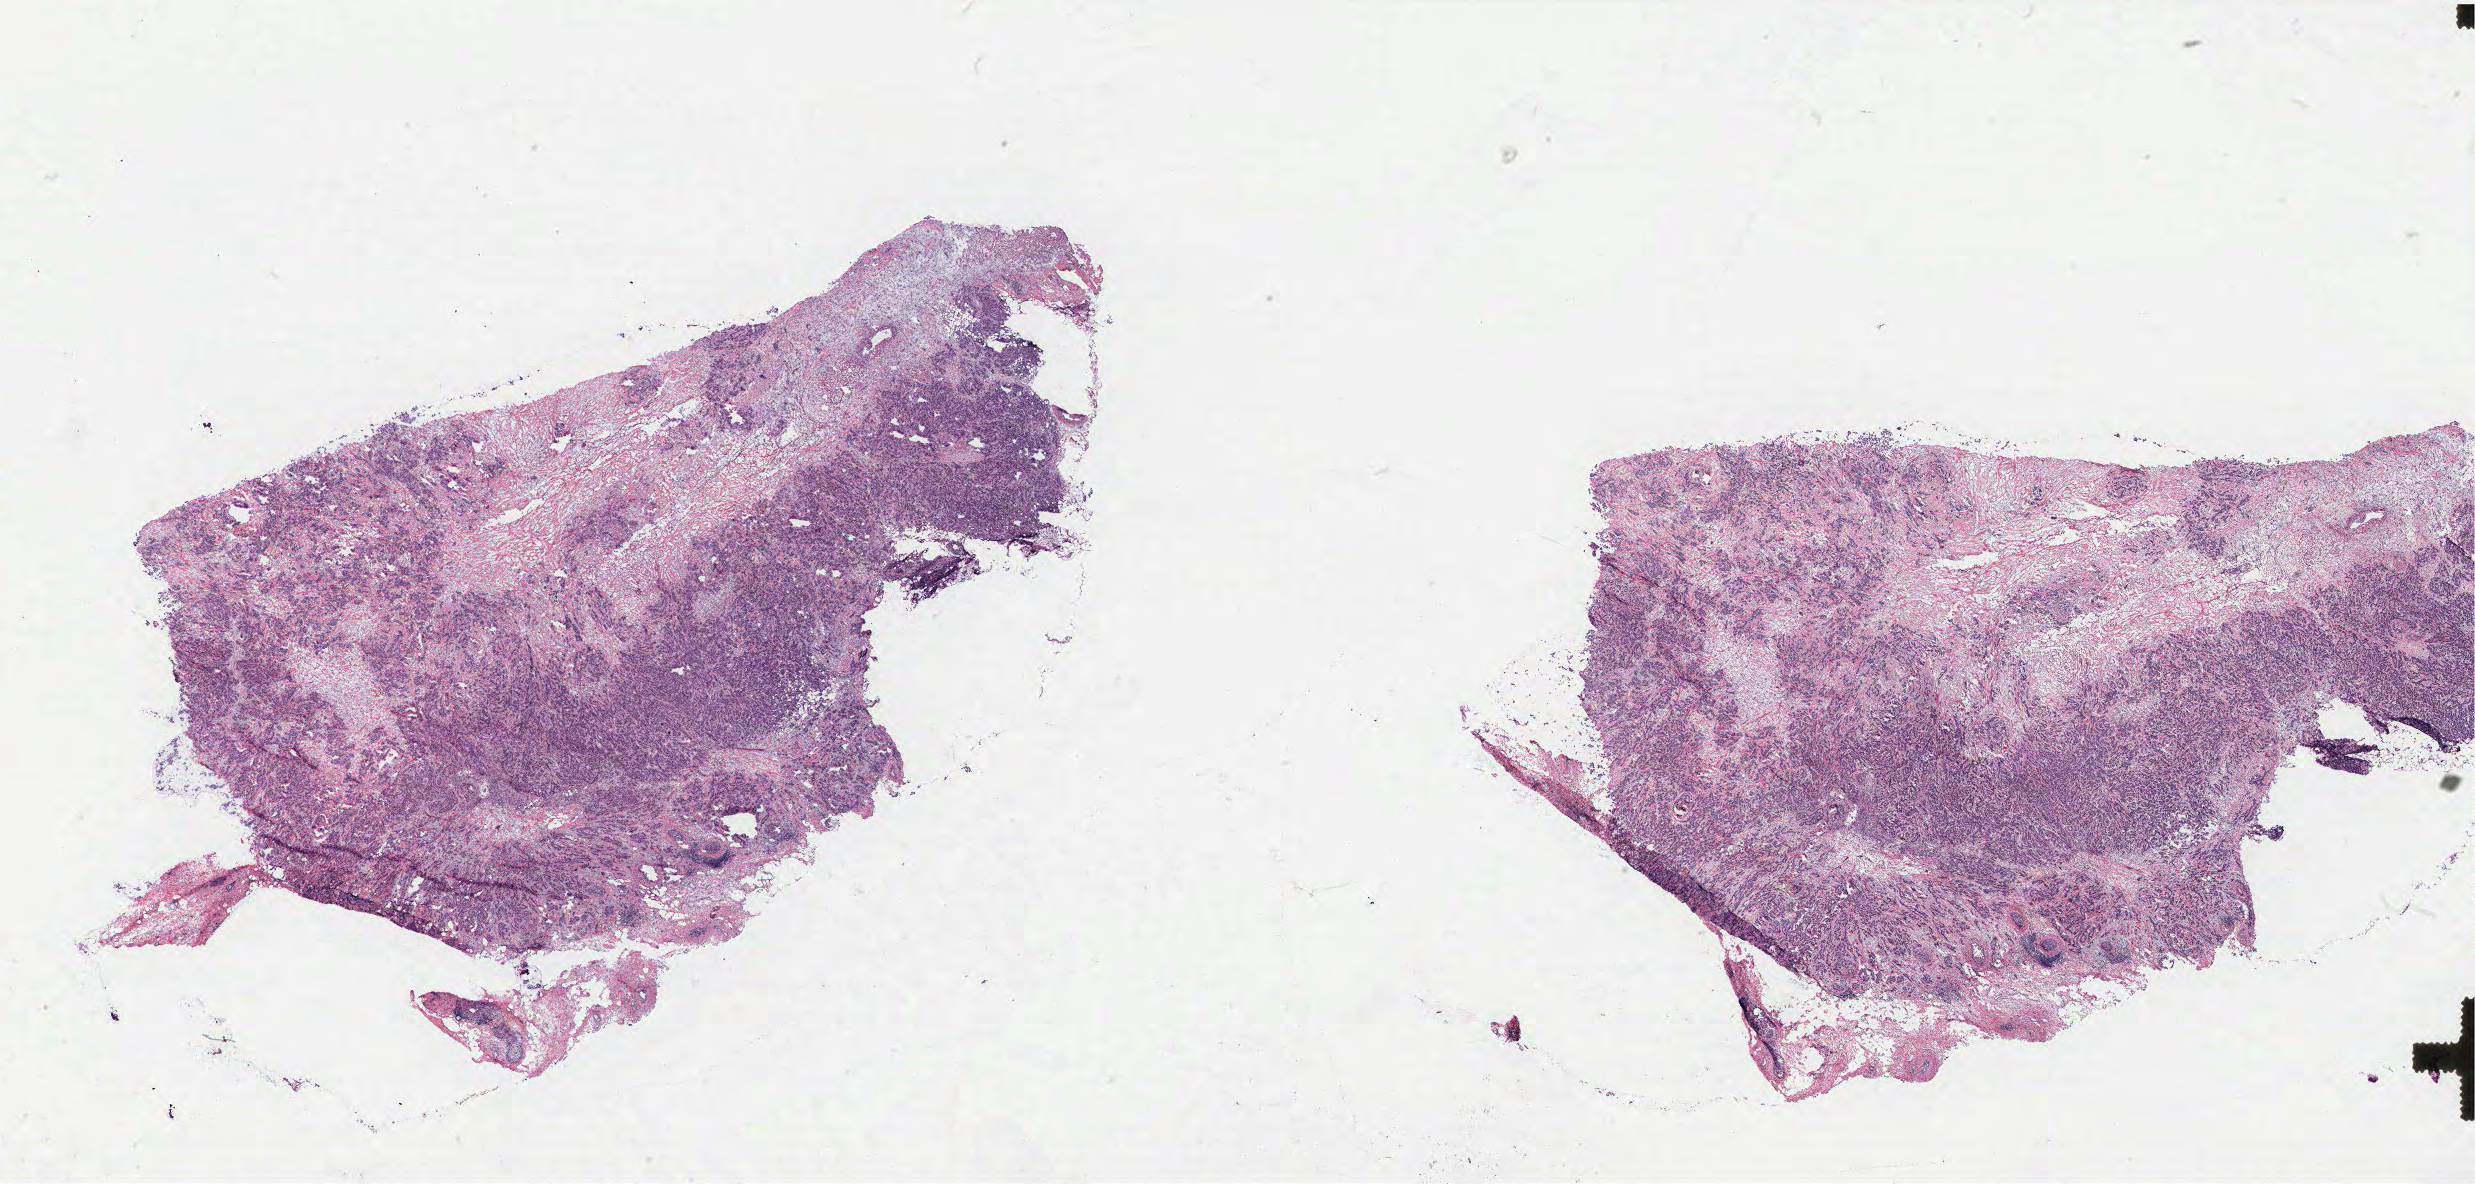
Whole-slide histology image, H&E-stained, shown as a low-resolution overview of the whole scanned area (about 39.6 x 19.0 mm, acquisition: 40x scan). Breast, tissue type not recorded. Patient: female, age 55 years.
Patient diagnosis: Infiltrating duct carcinoma, NOS.